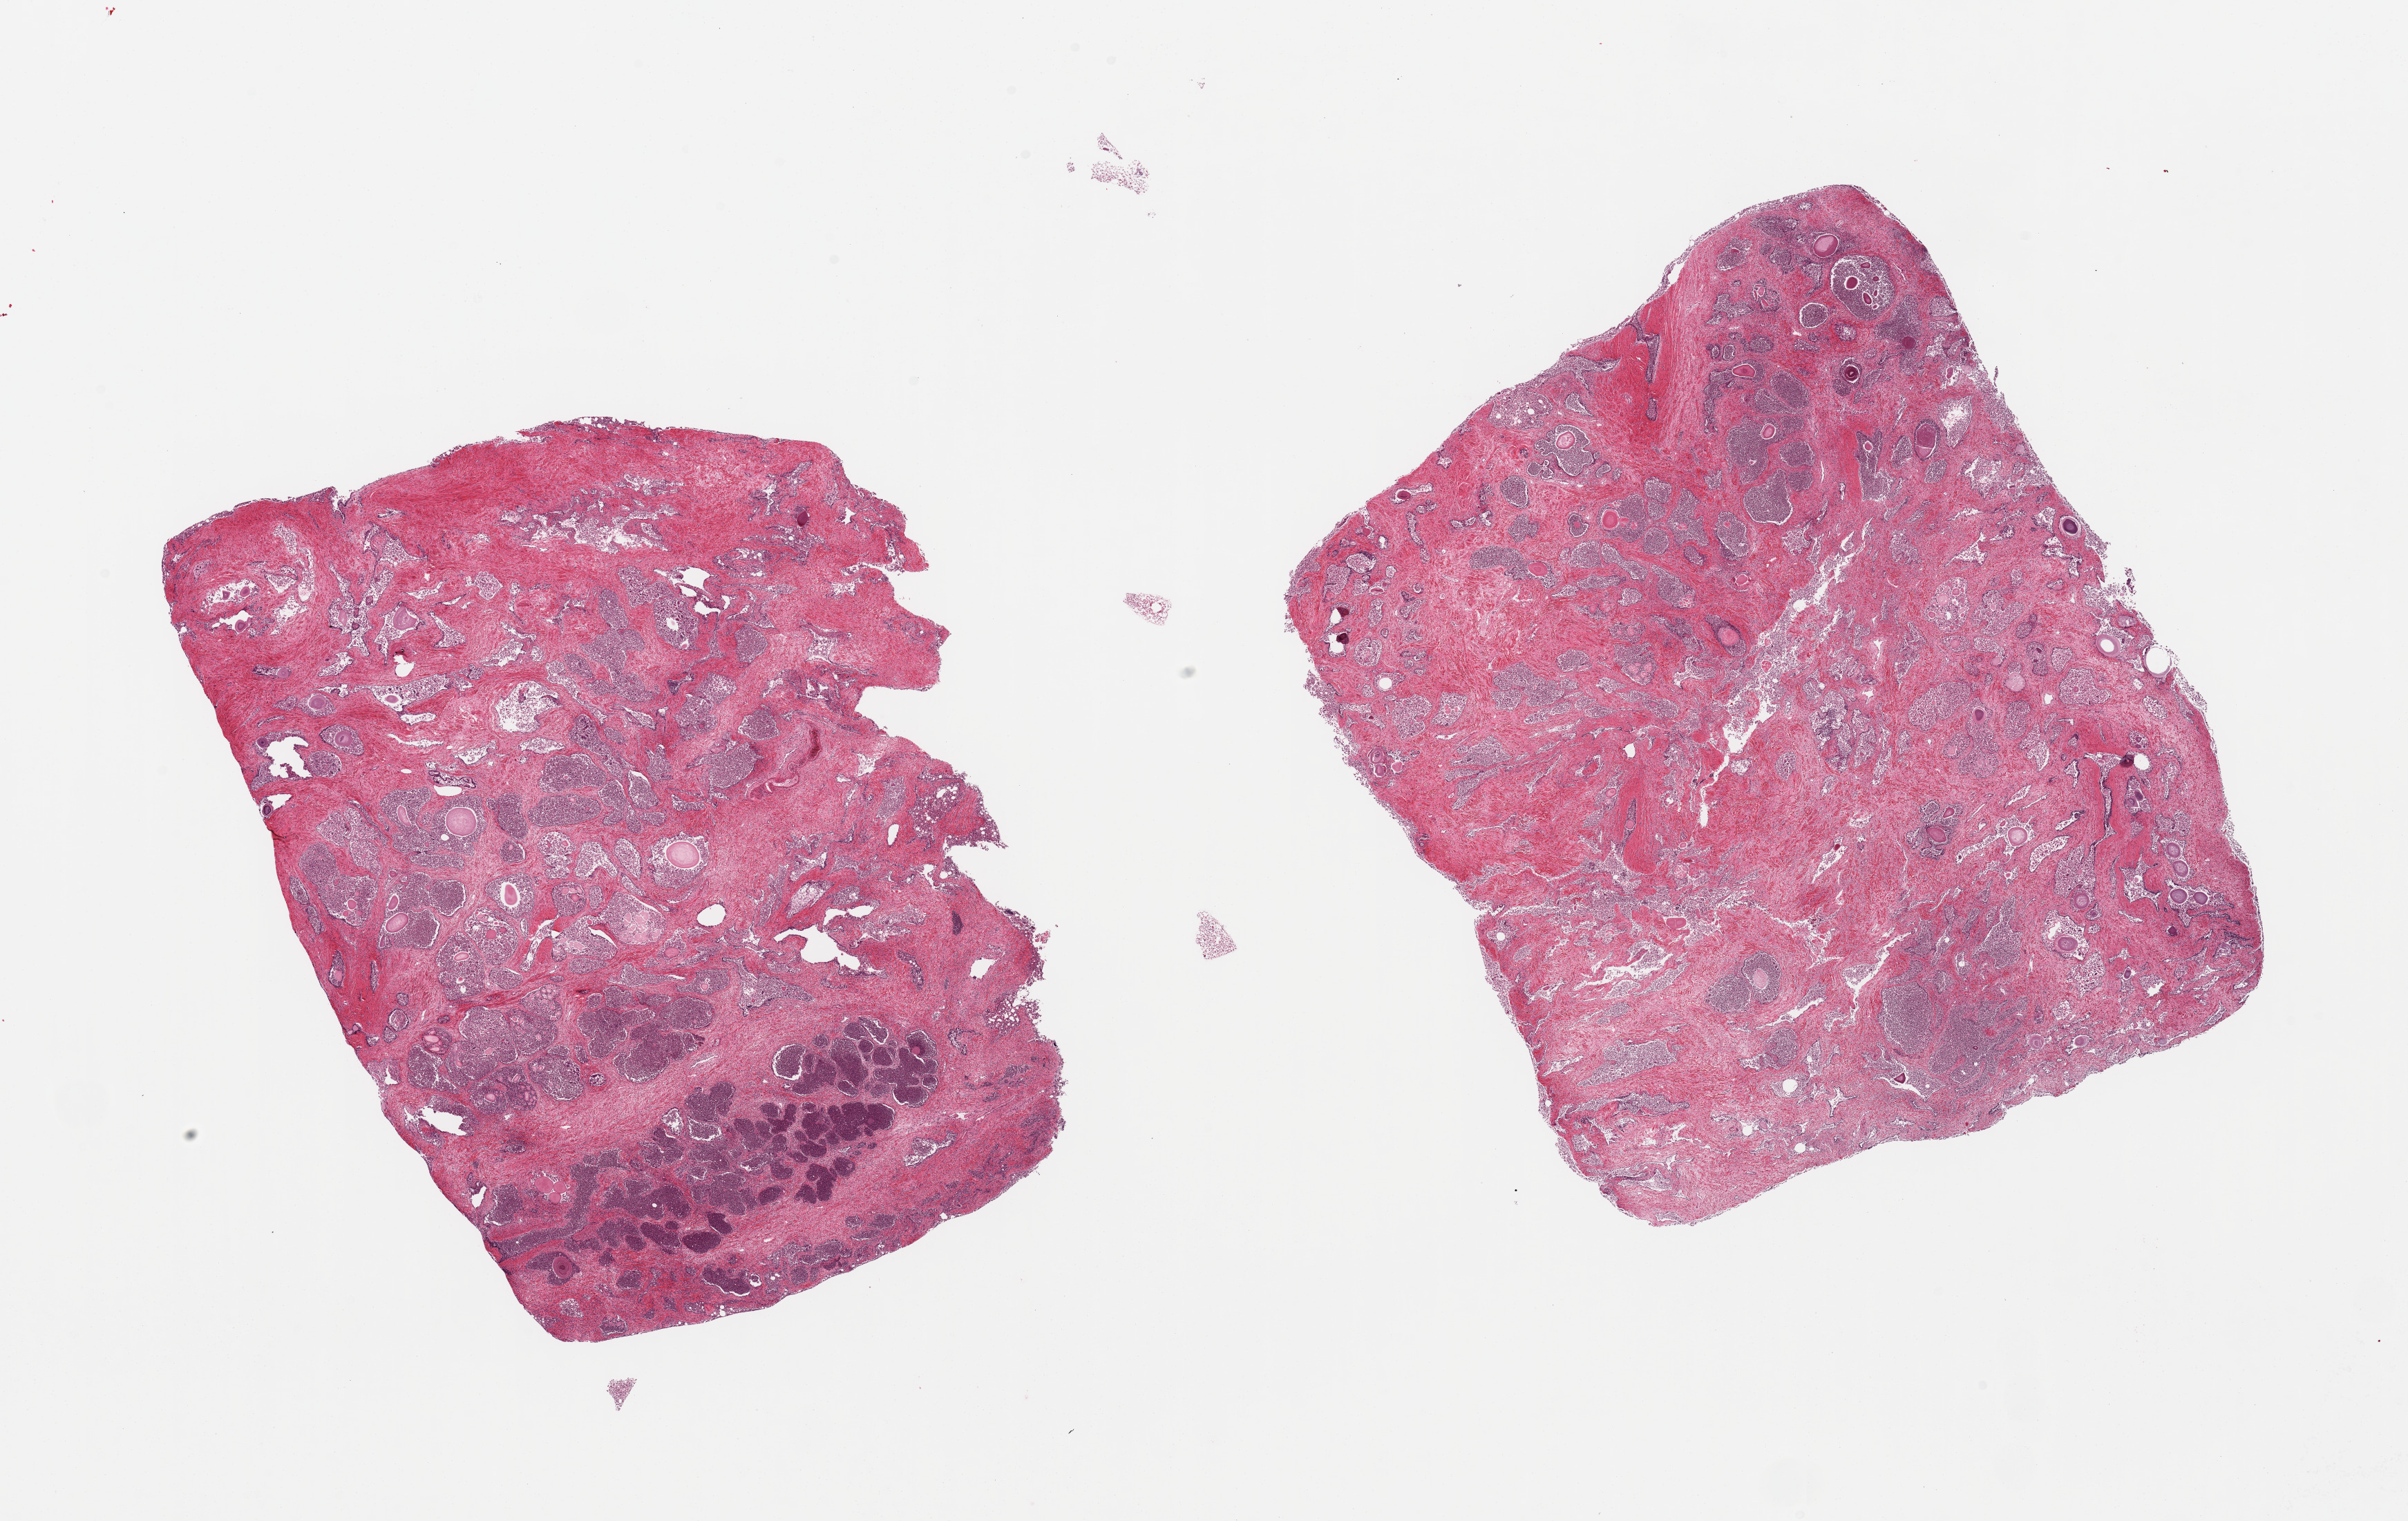
Whole-slide image, hematoxylin and eosin (H&E) stain, shown as a low-resolution overview of the whole scanned area (about 27.6 x 17.4 mm, acquisition: 20x scan), PAXgene-fixed paraffin-embedded (PFPE) section, sampled site (target tissue): prostate, tissue donor sample. Male donor.
Review note (as recorded): 2 pieces, glandular elements with advance autolysis; prostatic abscesses with abundant polymorphonuclear leukocytes distending many lumina.